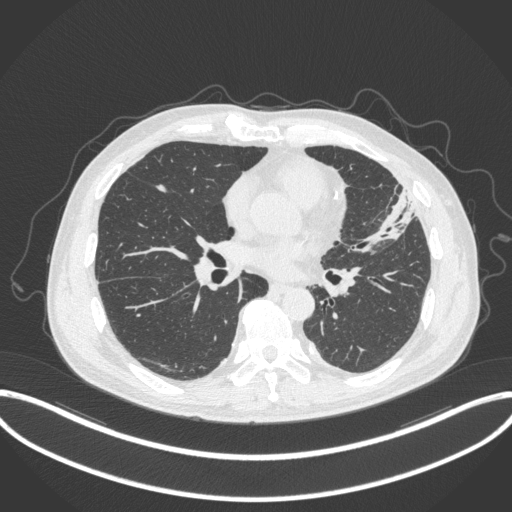
Chest CT, one axial slice; position 157 of 382 along the scan axis; reconstruction kernel B31f; lung window (W 1500 / L -600 HU); 1 mm slice thickness; 512 × 512 image matrix. Male patient, age 64 years. From the clinical record (not read from this slice): clinical TNM (as recorded): T4 N1 M0; histopathological grade: G3.
Structures marked on this image (bounding box drawn by a radiologist):
- lung tumour (recorded histology: adenocarcinoma): bounding box [x1, y1, x2, y2] px = [363, 183, 415, 253]